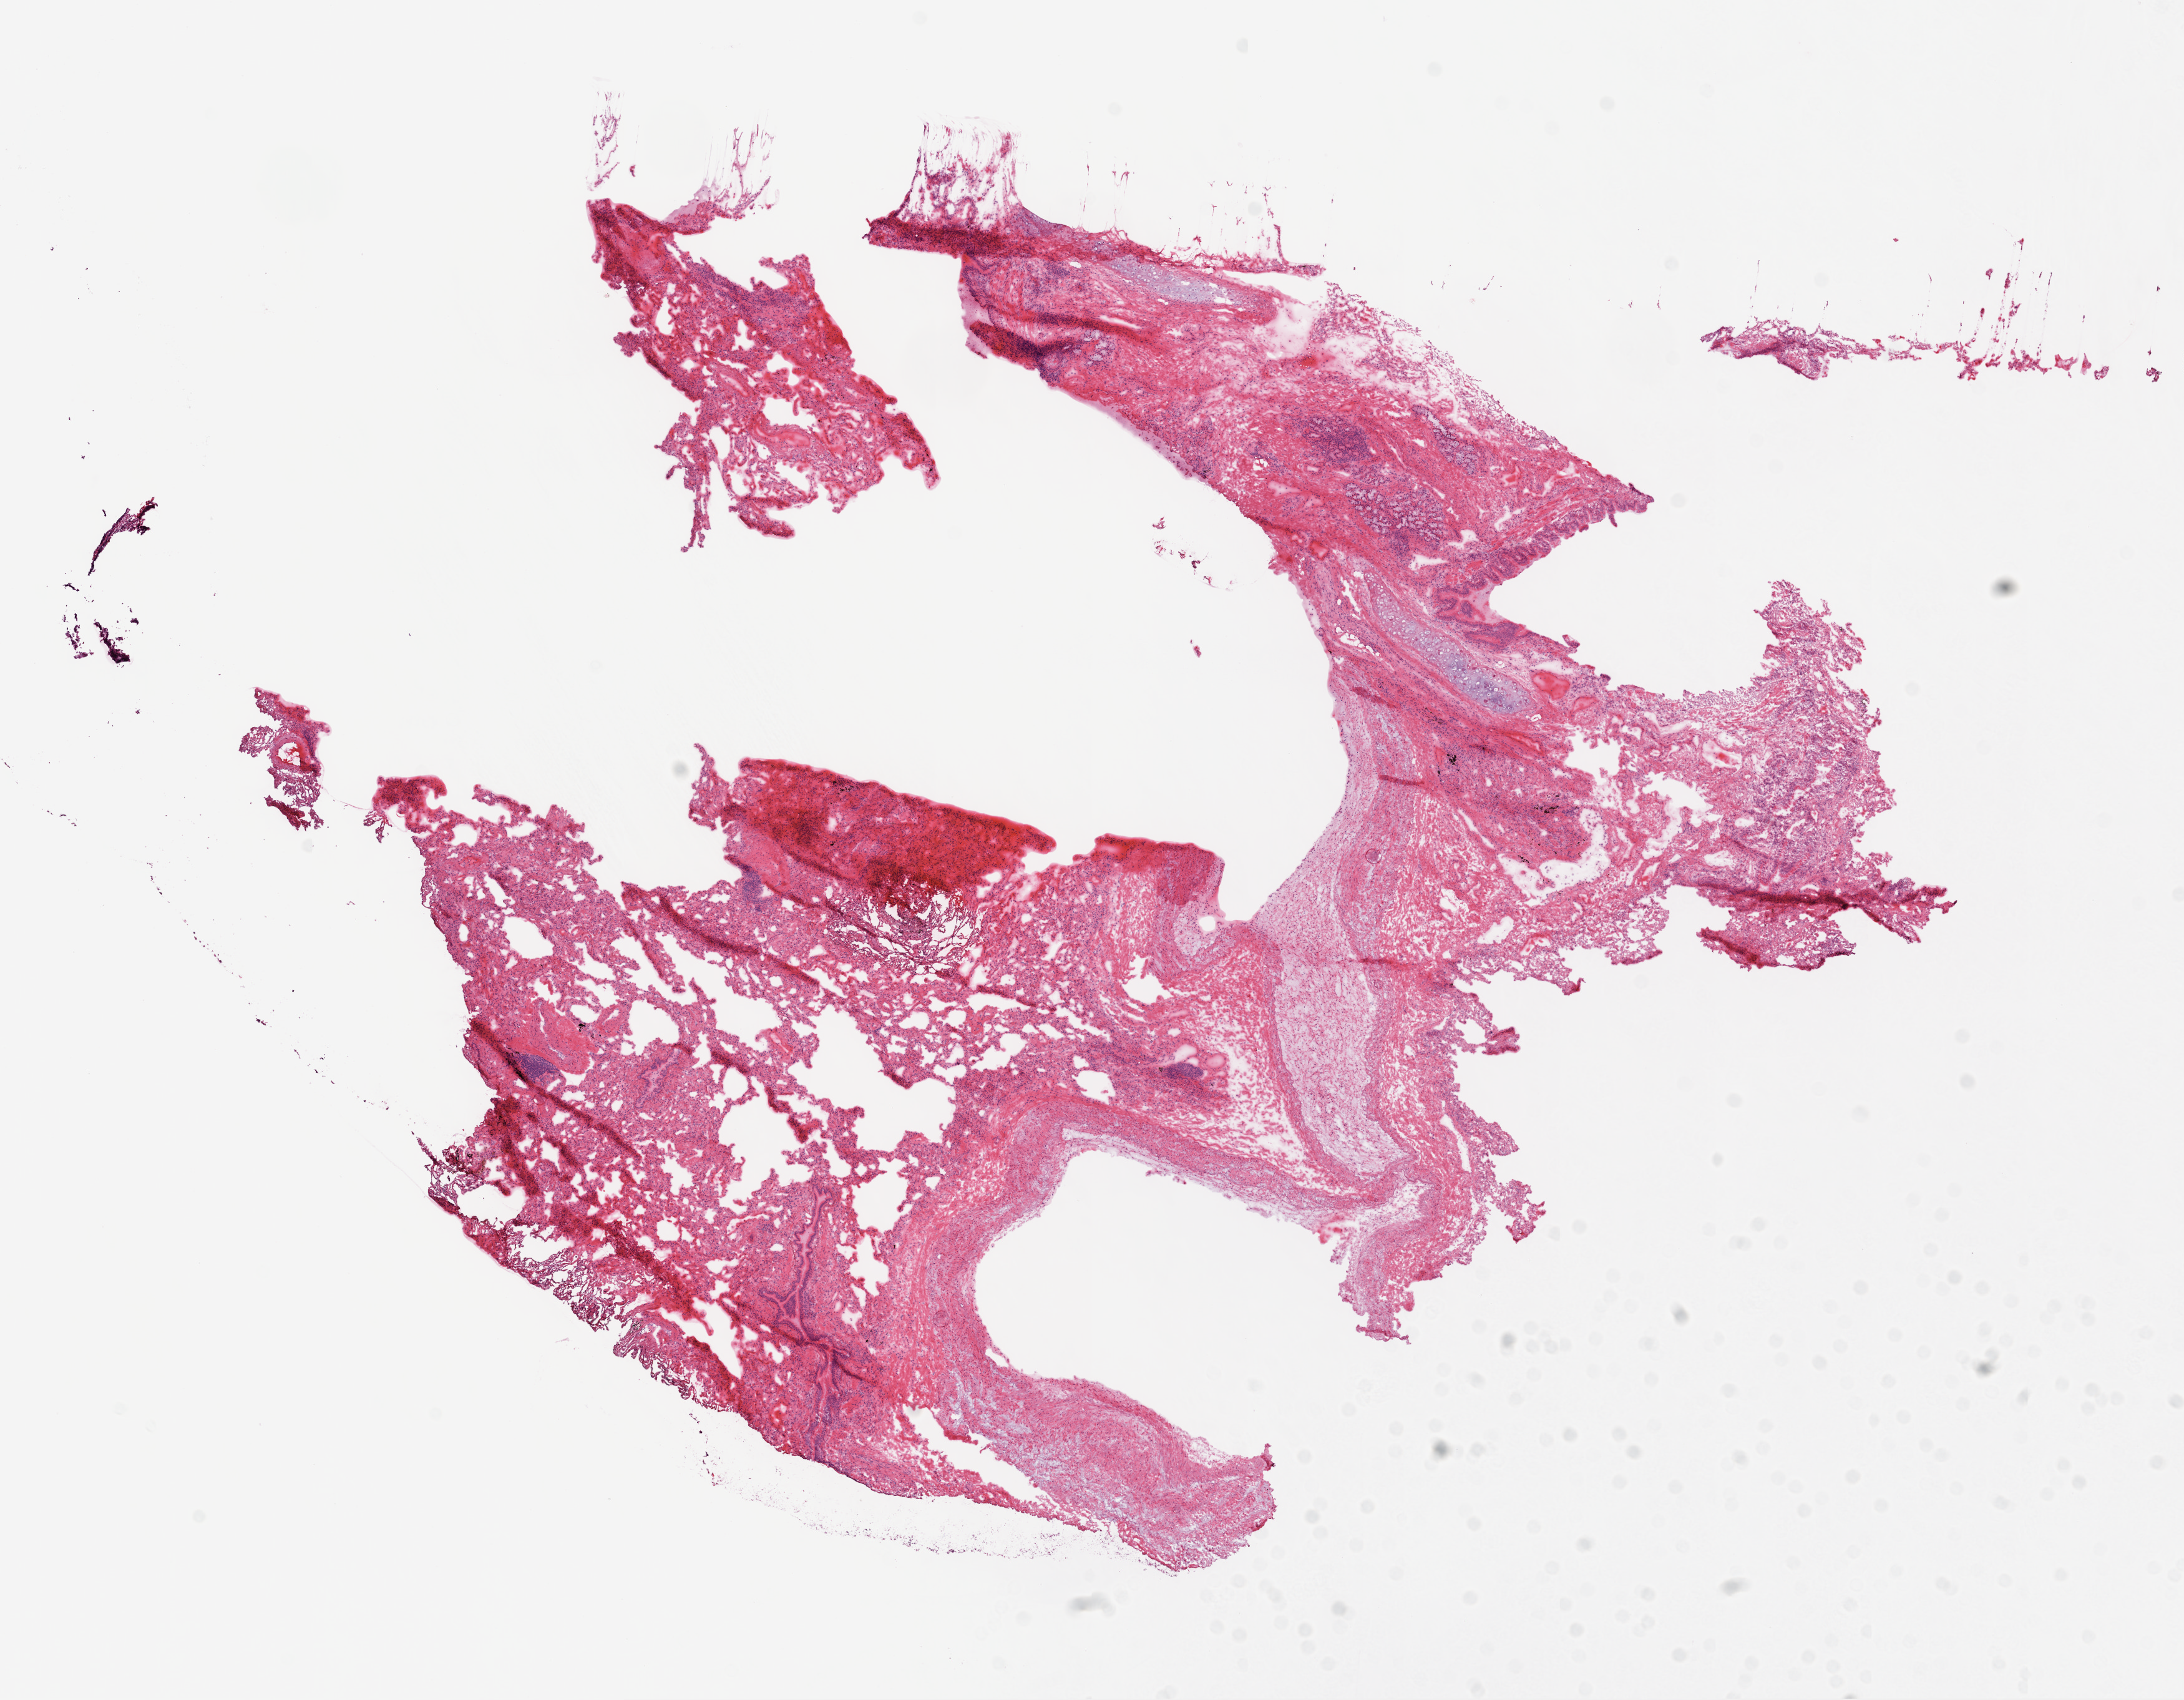
Digitized Hematoxylin and eosin (H&E) stained tissue section (whole slide) — a low-resolution overview of the entire scanned area, about 14.0 x 10.9 mm, frozen section from the top of the tissue portion, sample: solid tissue normal (non-tumour tissue), lung. Patient: male, age at initial diagnosis 64 years.
This section: solid tissue normal sample (biorepository sample class). Patient diagnosis: Squamous cell carcinoma, NOS (lower lobe, lung).